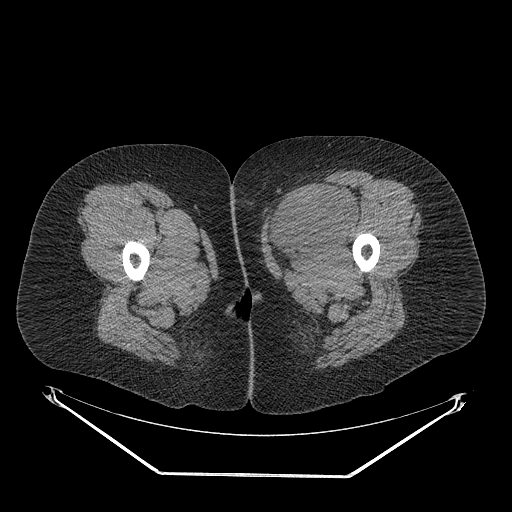
CT of an extremity soft-tissue mass (from a PET/CT study), one axial slice; position 30 of 267 along the scan axis; reconstruction kernel STANDARD; soft-tissue window (W 400 / L 40 HU); 3.75 mm slice thickness; 512 × 512 image matrix. Female patient. Case-level facts recorded for this patient, not image findings: histological type: myxofibrosarcoma; grade: intermediate; site of the primary tumour: left thigh.
Structures marked on this image (expert contour drawn on MRI and transferred to this co-registered scan by the dataset authors):
- gross tumour volume including surrounding oedema: bounding box <265,189,359,261> (left, top, right, bottom; pixels)
- gross tumour volume (mass): <267,187,355,250>